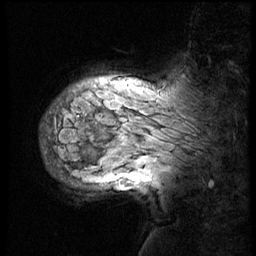
Breast MRI (dynamic contrast-enhanced), one sagittal slice. Position 44 of 56 along the scan axis. 3 images stored at this slice position (order not interpretable as contrast timing). 1.5 T. TE 4.2 ms, TR 8.9 ms. 3 mm slice thickness. 256 × 256 image matrix, field of view 220 × 220 mm. Patient: female, 57 years. From the clinical record (not read from this slice): setting: breast cancer imaged before/during neoadjuvant chemotherapy; receptor status: HER2-positive.
Structures marked on this image (semi-automatically segmented with operator editing):
- analysis volume of interest (the breast-tissue region the enhancement analysis was run in; not a lesion): bounding box <41,70,228,156> (left, top, right, bottom; pixels)
- tumour enhancement mask (voxels above the 140 % enhancement threshold inside the analysis volume of interest): <112,82,132,84>